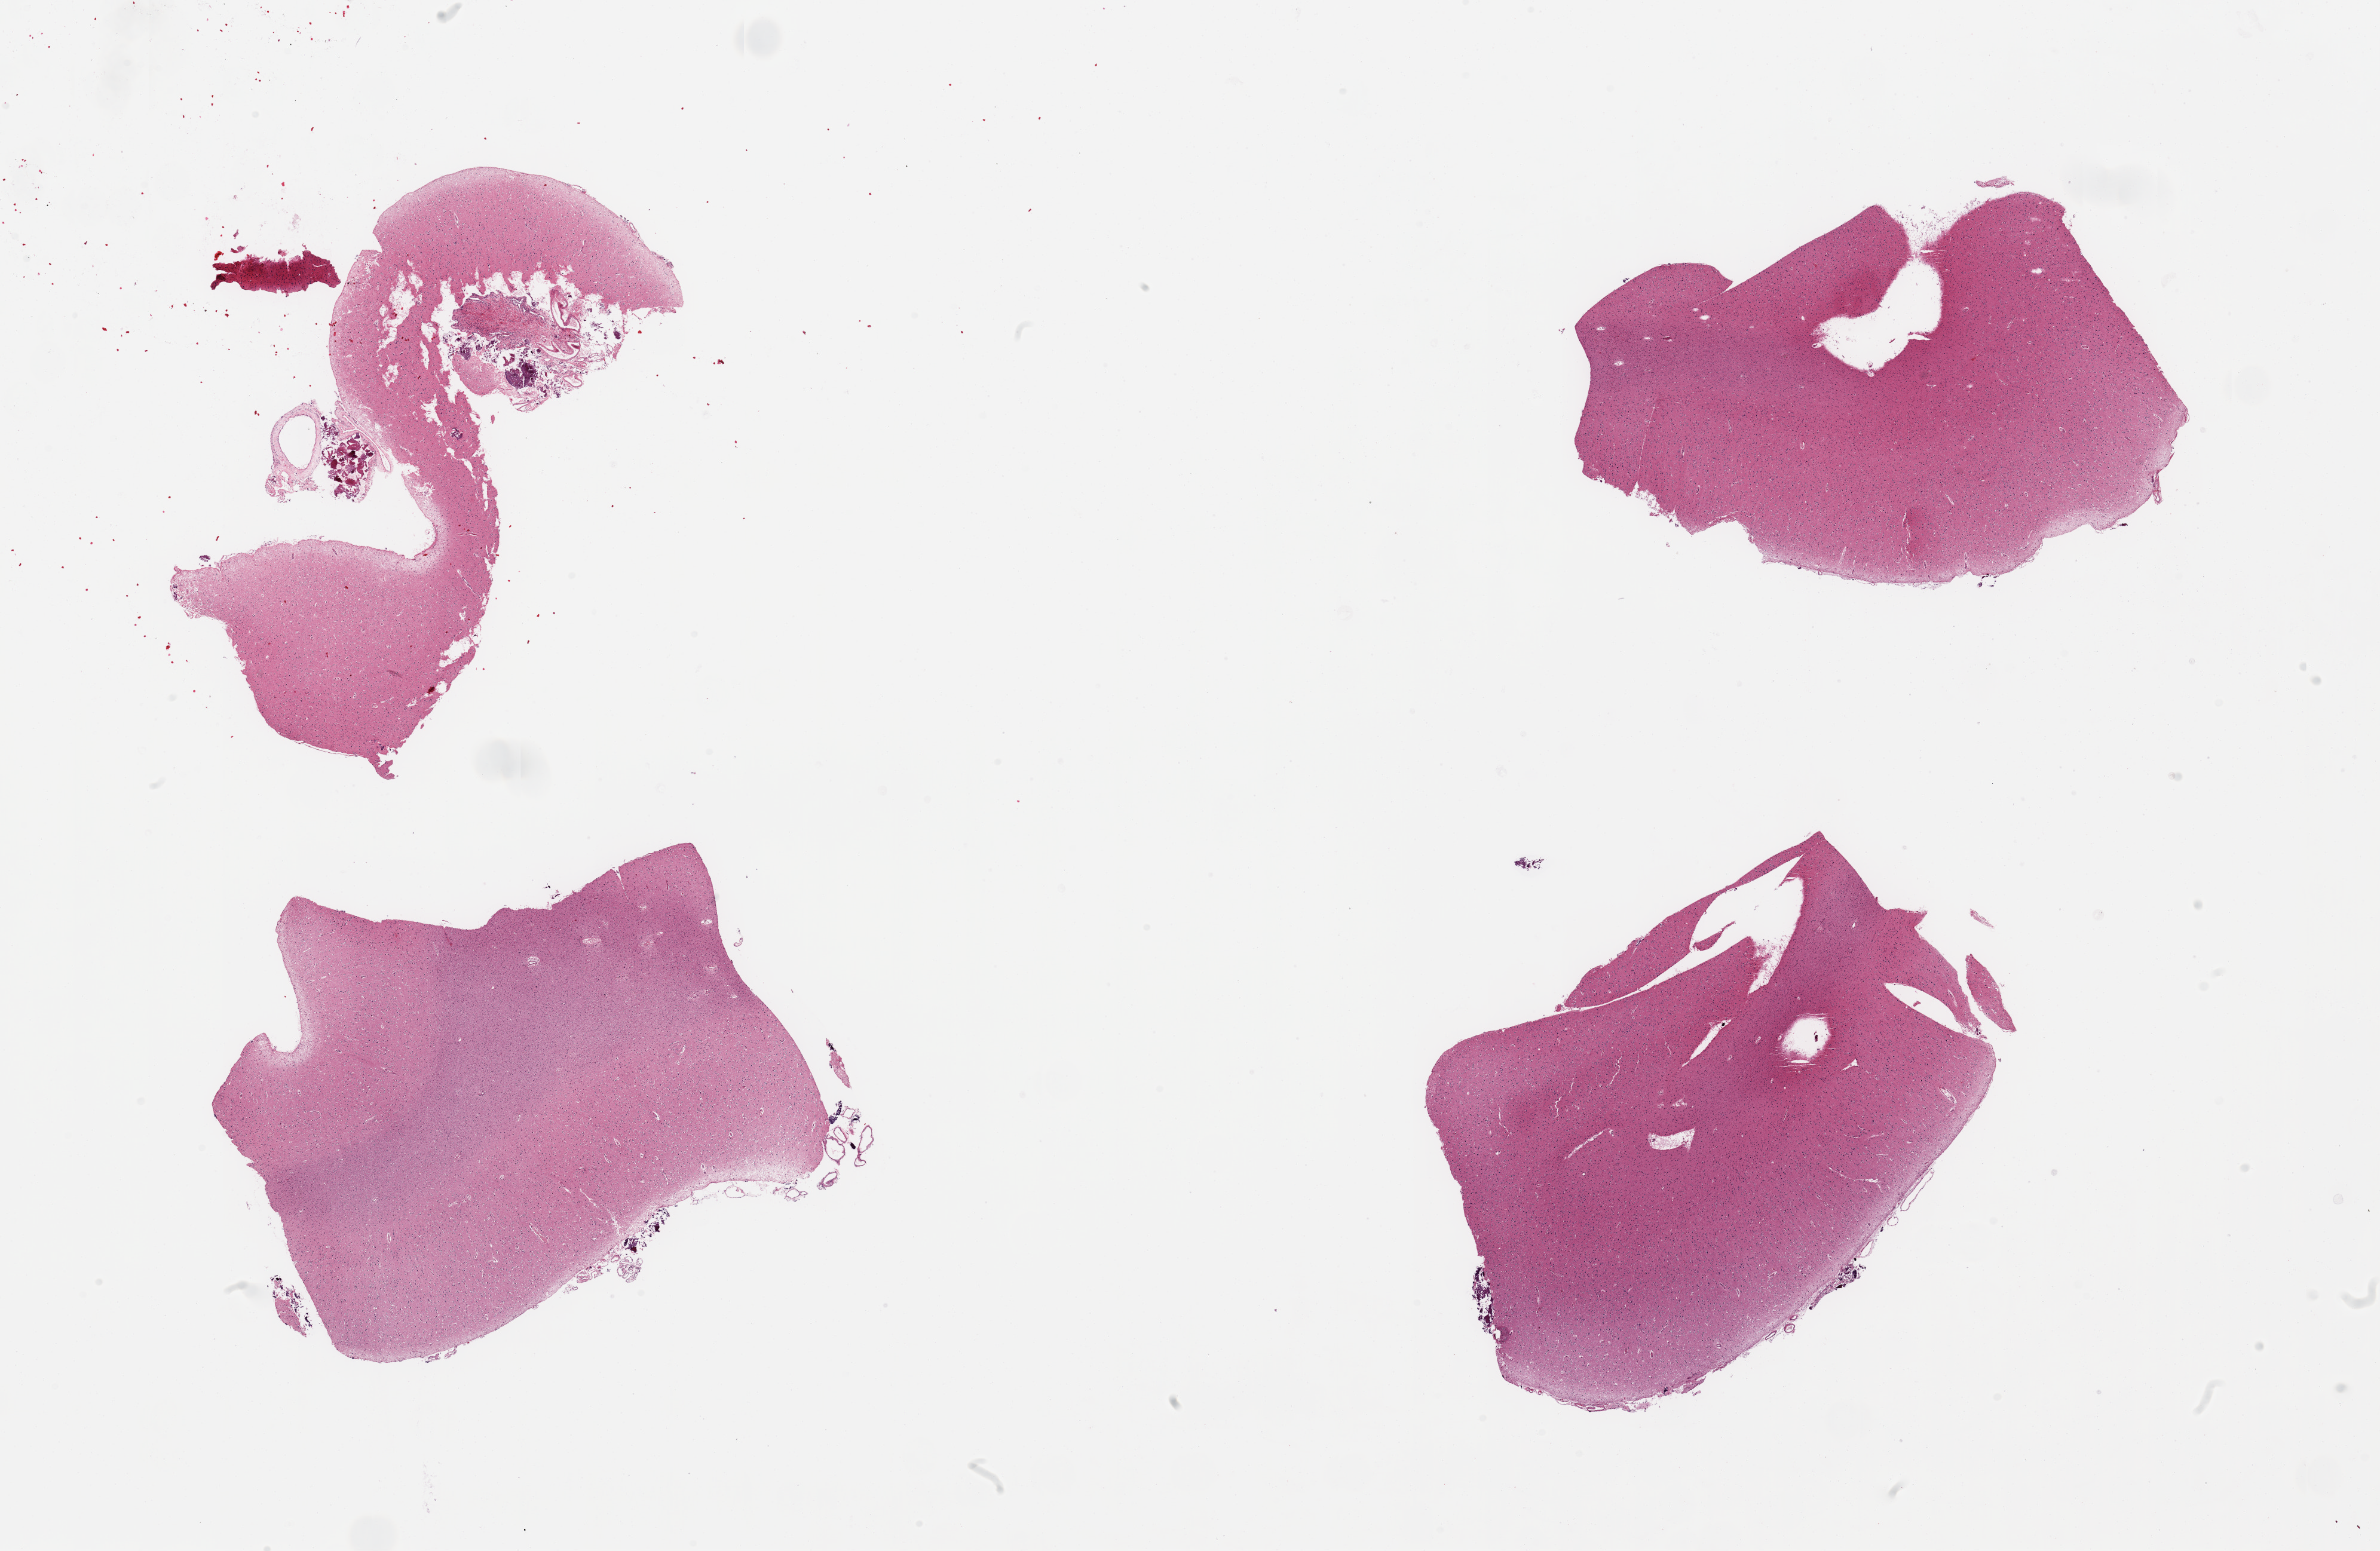
Whole-slide image, H&E stain, brightfield, a low-resolution overview of the entire scanned area, about 31.5 x 20.5 mm (slide scanned at 20x). PAXgene-fixed, paraffin-embedded tissue. Target tissue: cerebral cortex. Tissue donor sample.
Pathologist's review note for this sample: 4 pieces, no abnormalities.